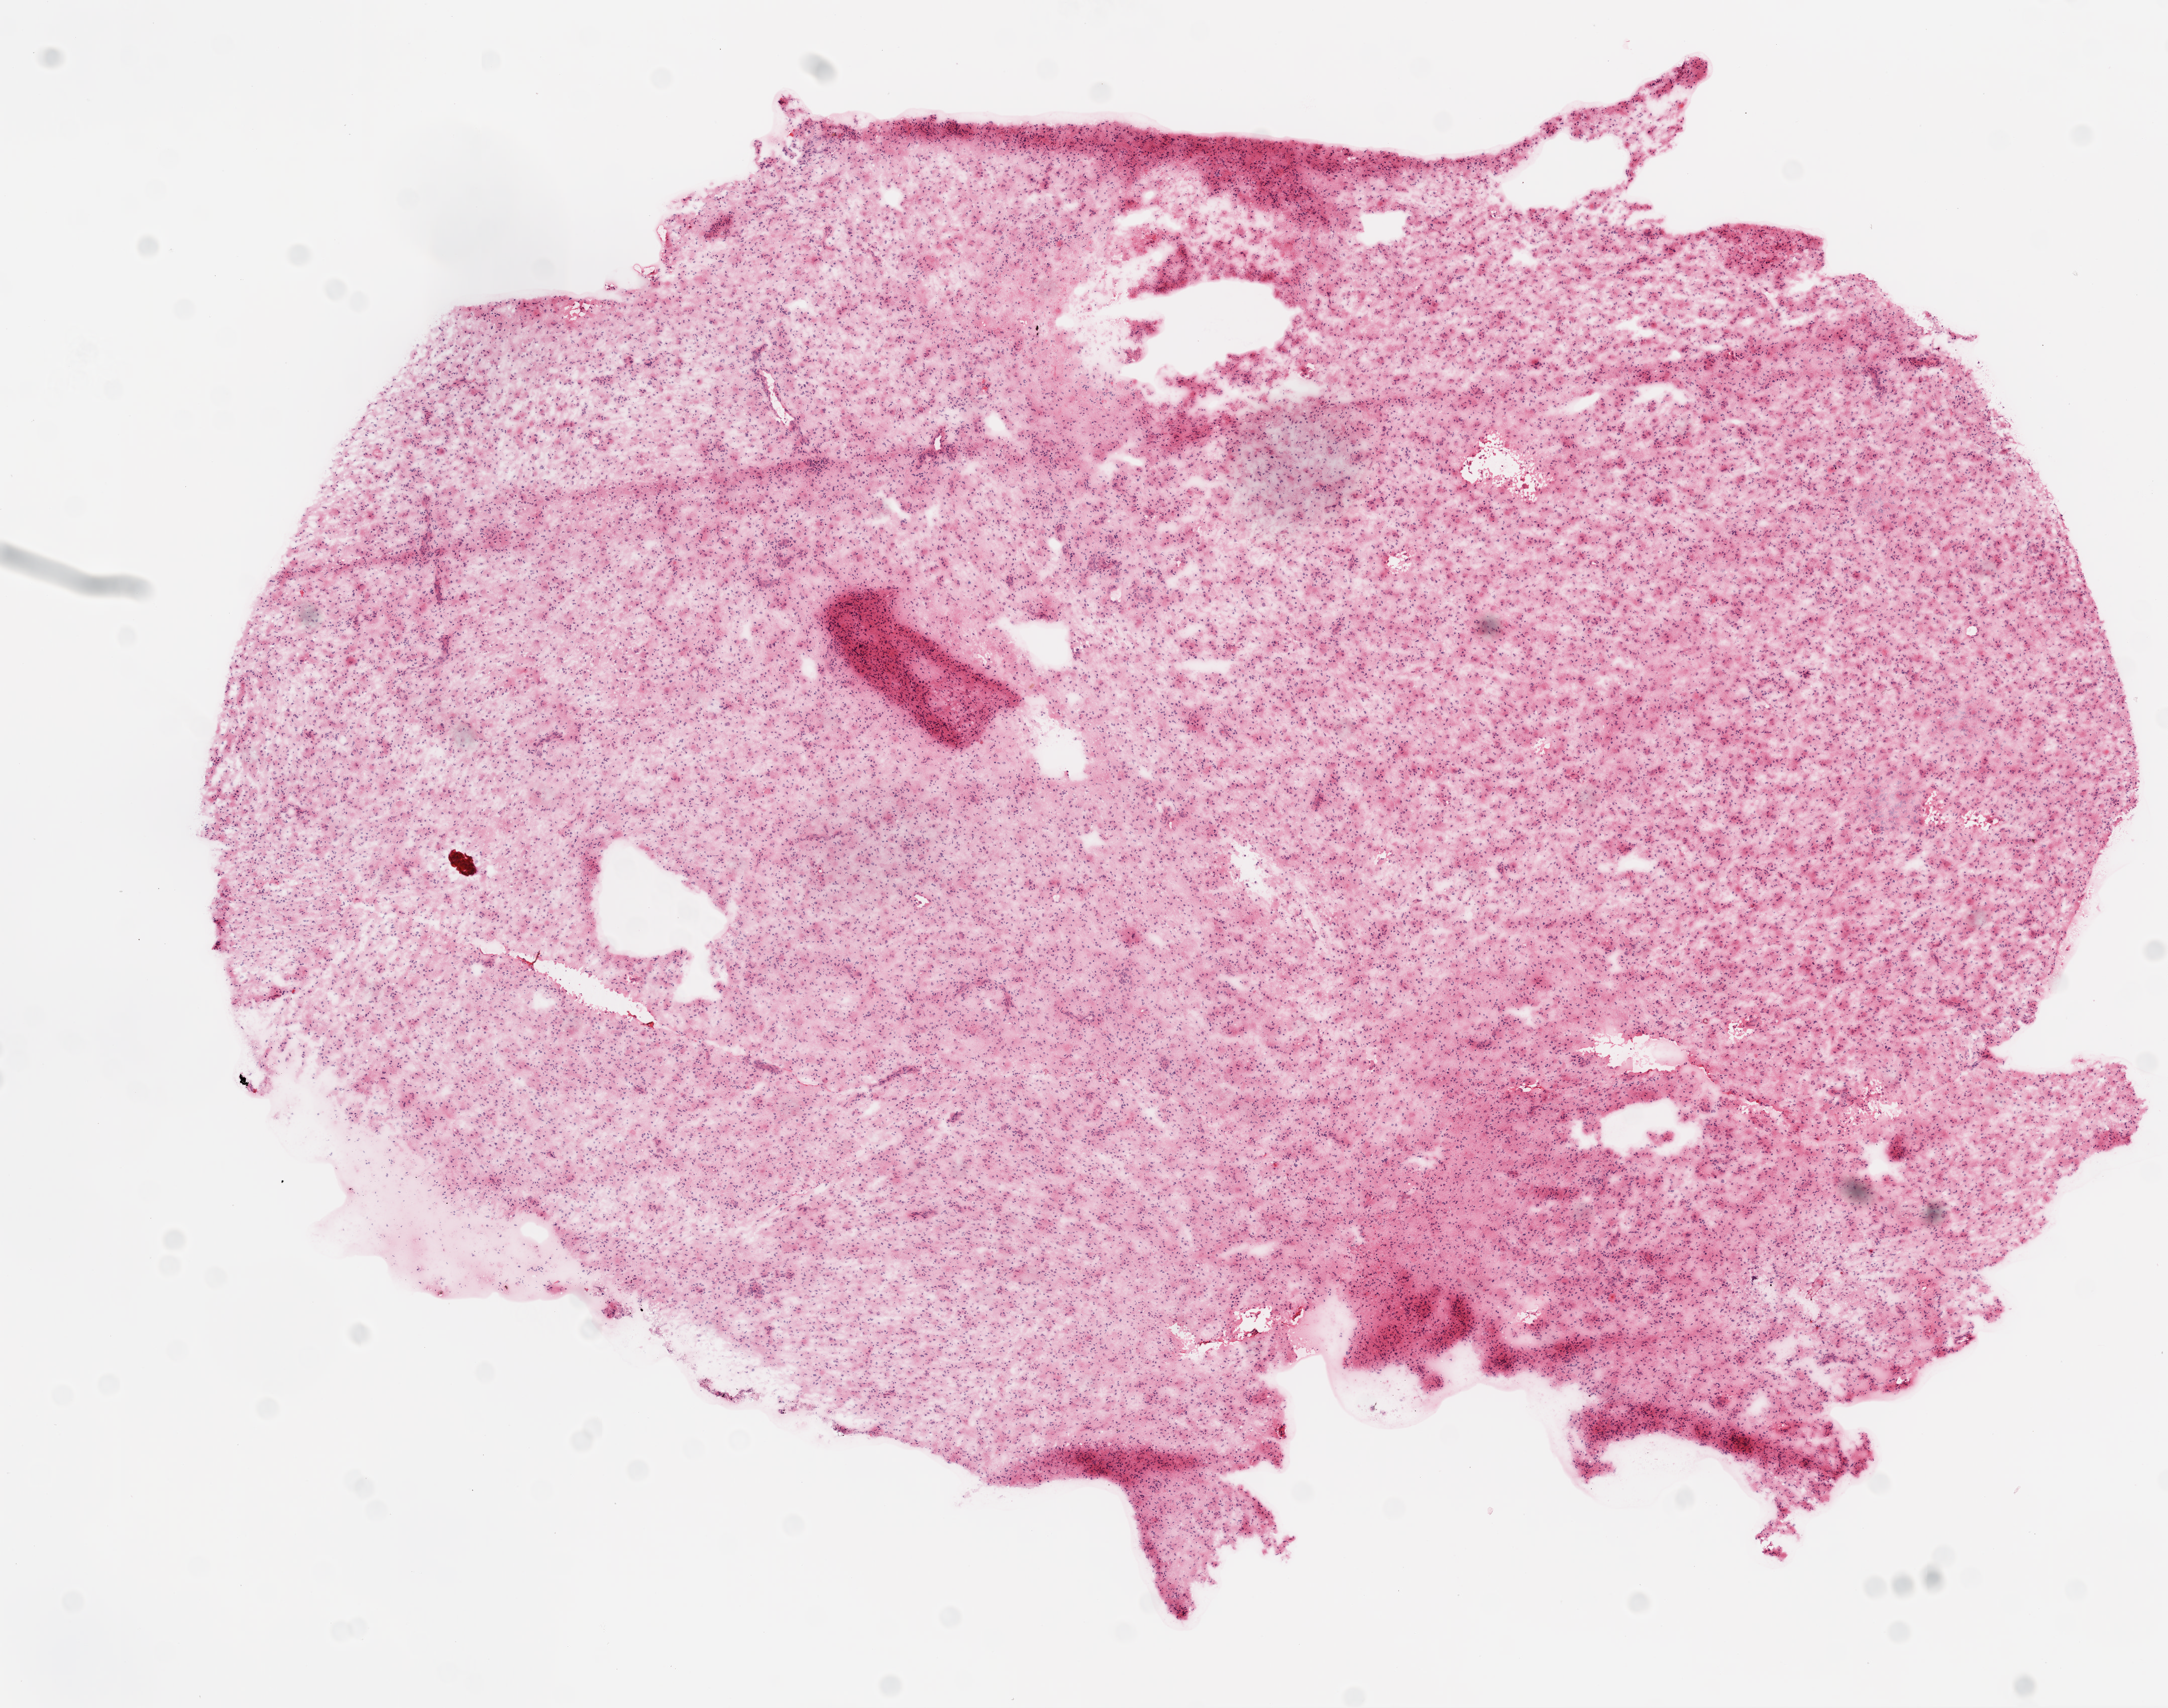
Whole-slide histology image, Hematoxylin and eosin (H&E) stained, shown as a low-resolution overview of the whole scanned area (about 8.7 x 6.9 mm); frozen section from the bottom of the tissue portion; sample: primary tumour, brain. Female, age 71 years at initial diagnosis. Slide review estimates, as recorded: tumour cells 80%, tumour nuclei 85%, normal cells 0%, stromal cells 20%, necrosis 0%.
Pathologic diagnosis: Glioblastoma.